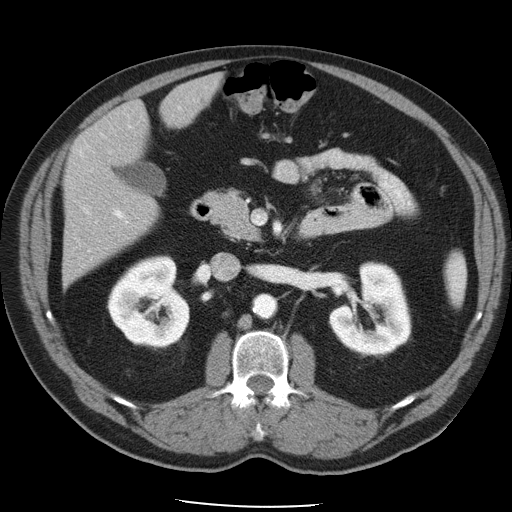
Contrast-enhanced abdominal CT, one axial slice; reconstruction kernel STANDARD; 120 kVp; intravenous contrast given; soft-tissue window (W 400 / L 40 HU); 5 mm slice thickness; 512 × 512 image matrix, field of view 395 × 395 mm. Male patient, age 68 years. Case-level facts recorded for this patient, not image findings: diagnosis: colorectal cancer liver metastases, imaged before liver resection; multiple liver metastases: yes; largest metastasis: 1.7 cm; chemotherapy before resection: yes.
Structures marked on this image (manually delineated by an expert):
- hepatic veins: bounding box (x1, y1, x2, y2) in pixels: (83, 209, 98, 223)
- liver: (63, 76, 222, 282)
- planned liver remnant (the part of the liver to remain after resection): (66, 76, 221, 247)
- portal vein (with intrahepatic branches): (89, 101, 196, 252)